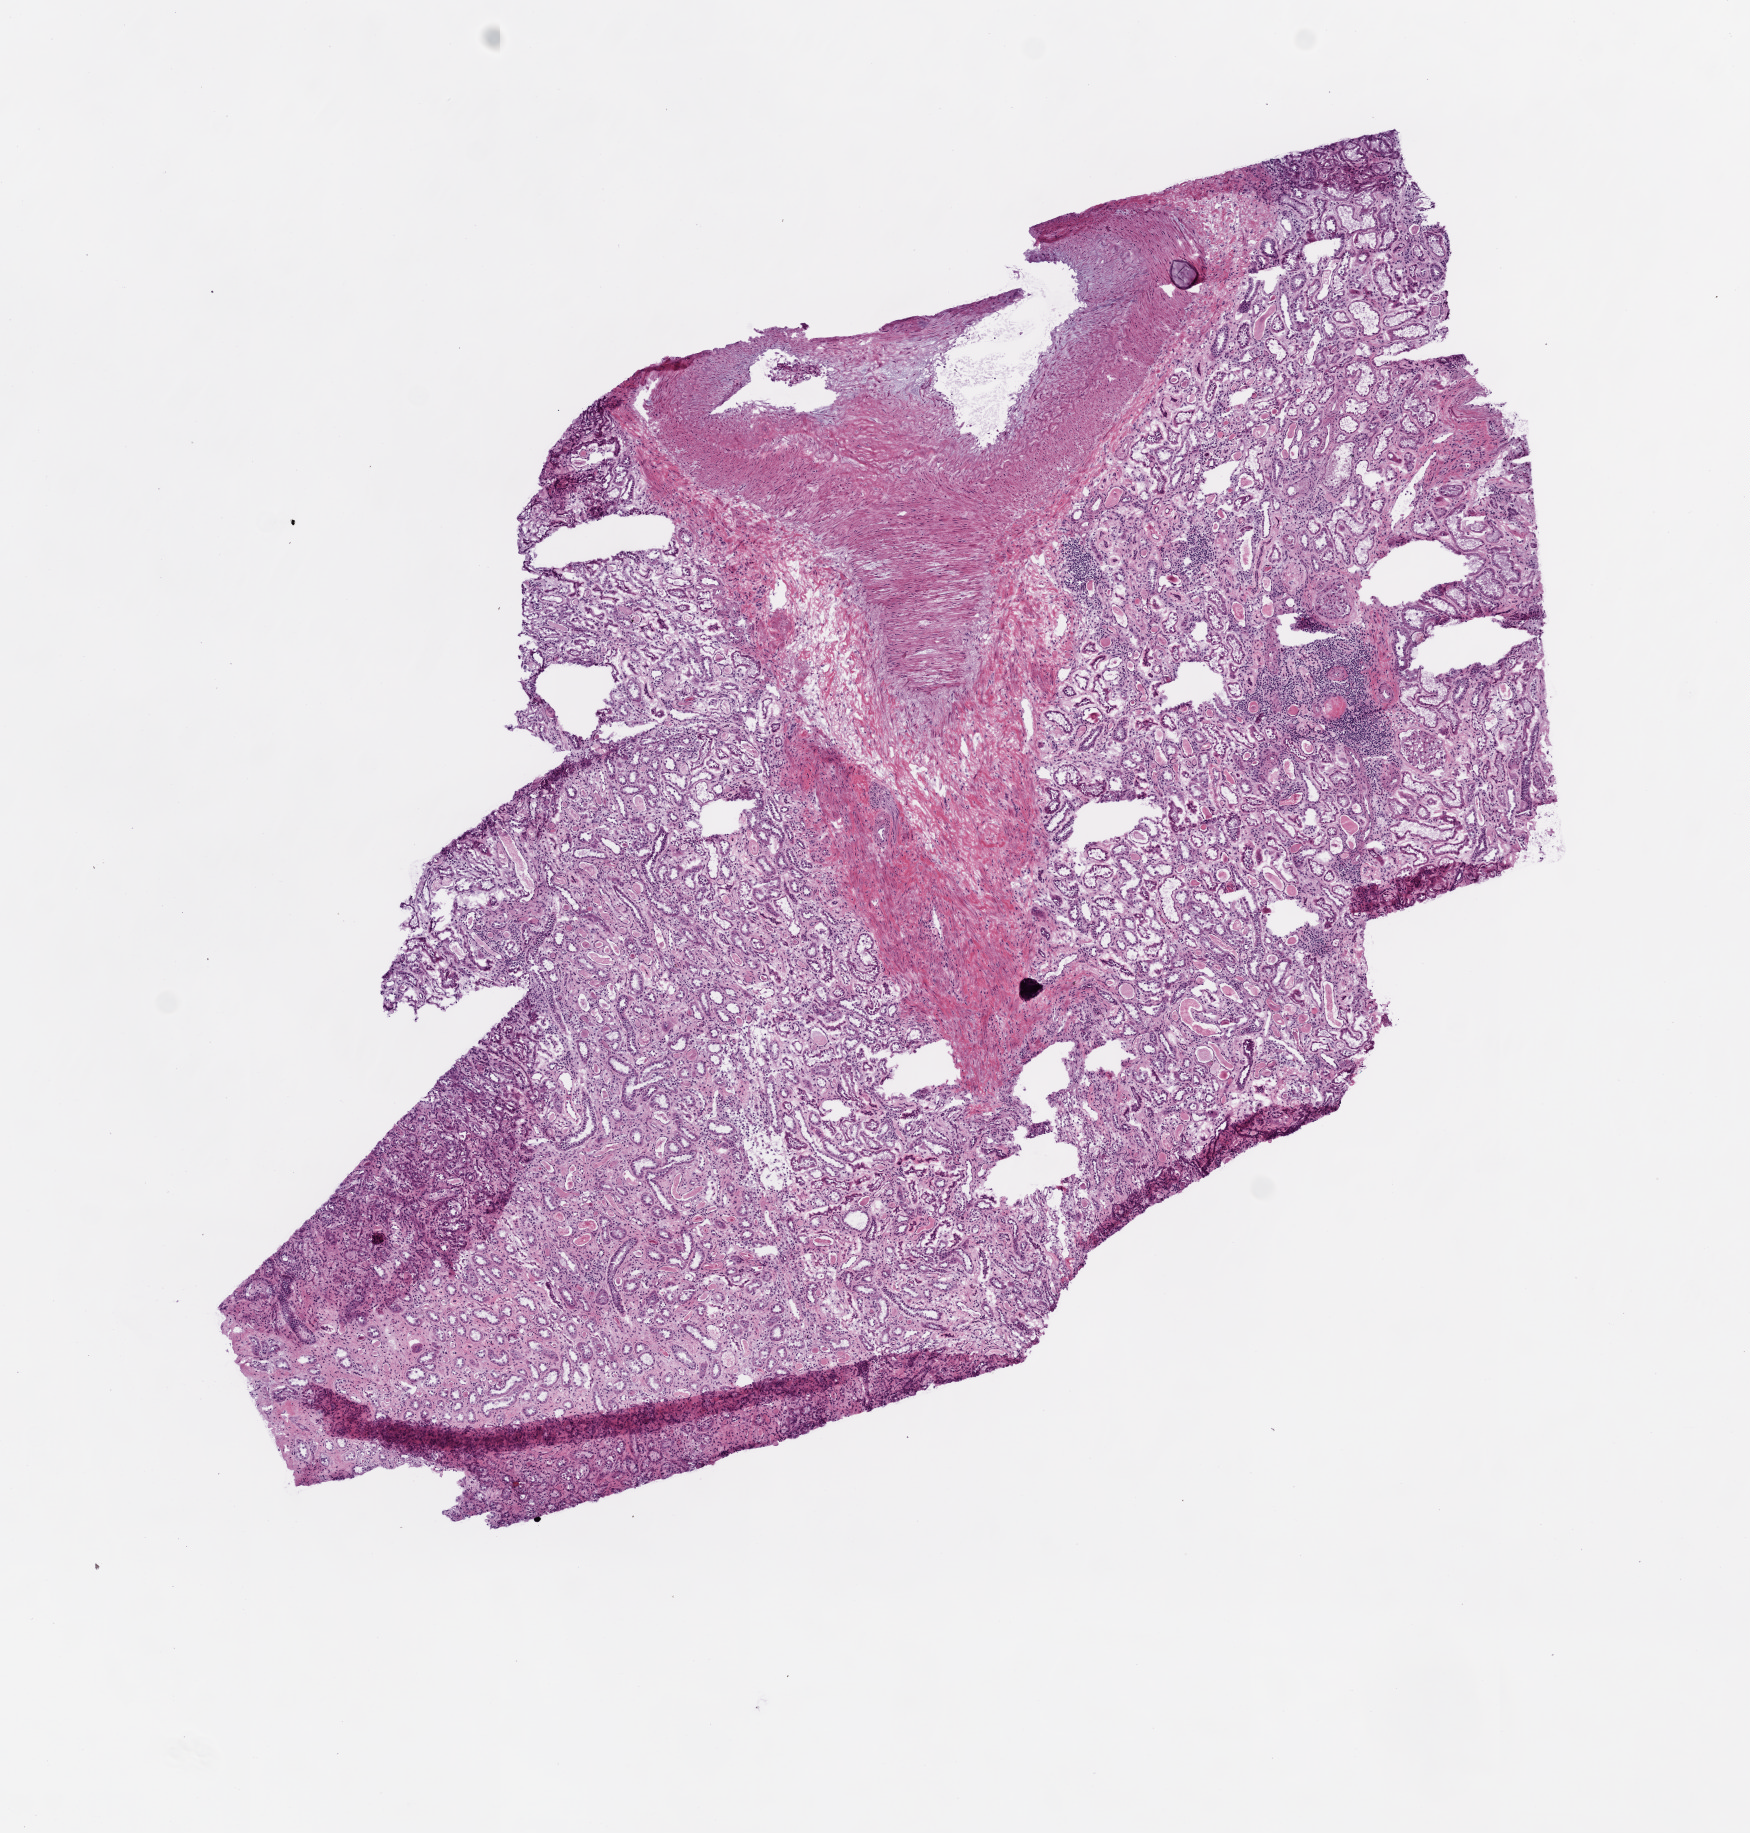
H&E-stained whole-slide image, low-resolution overview of the scanned area, about 7.0 x 7.4 mm (acquisition: 20x scan); frozen section; kidney, solid tissue normal (non-tumour tissue) sample. Female patient; age at initial diagnosis 65 years.
This section: solid tissue normal (non-tumour) sample from the same patient. Patient diagnosis: Clear cell adenocarcinoma, NOS.